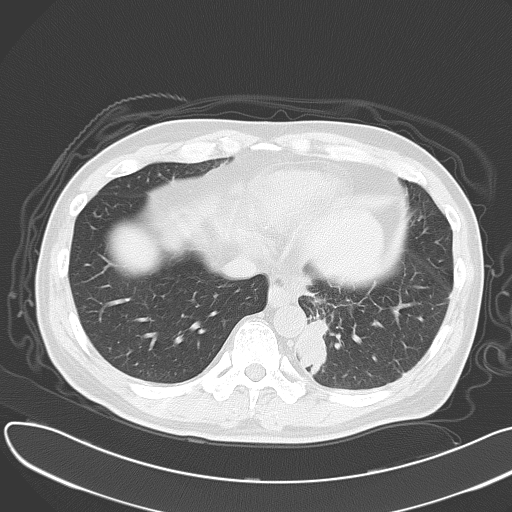
Chest CT, one axial slice. Slice 13 of 55 in the series (ordered by position). 120 kVp. Lung window (W 1500 / L -600 HU). 5 mm slice thickness. 512 × 512 image matrix, field of view 376 × 376 mm. Patient: male, 55 years. From the clinical record (not read from this slice): clinical TNM (as recorded): T2 N3 M0; histopathological grade: G3.
Outlined on this slice (rectangle marked by the reading radiologist):
- lung tumour (recorded histology: small cell carcinoma): bounding box <293,315,334,371> (left, top, right, bottom; pixels)